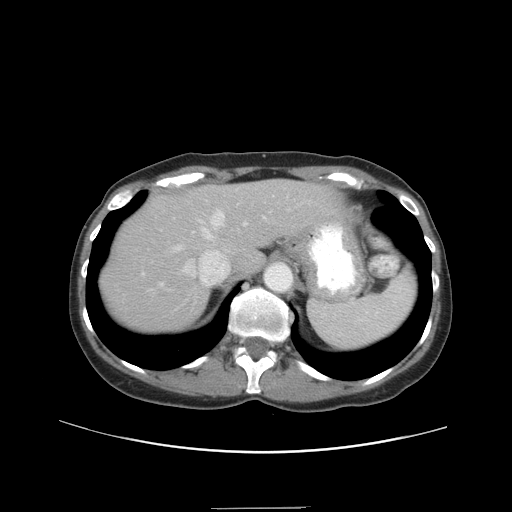
Contrast-enhanced abdominal CT, one axial slice. Slice 30 of 38 in the series (ordered by position). Intravenous contrast given. Soft-tissue window (W 400 / L 40 HU). 512 × 512 image matrix, field of view 388 × 388 mm. Female patient, age 64 years. Case-level facts recorded for this patient, not image findings: diagnosis: colorectal cancer liver metastases, imaged before liver resection; multiple liver metastases: no; largest metastasis: 3.8 cm.
Outlined on this slice (manually delineated by an expert):
- hepatic veins: box from (x=149, y=210) to (x=247, y=291) px
- liver: (x=103, y=182)–(x=338, y=331)
- planned liver remnant (the part of the liver to remain after resection): (x=147, y=182)–(x=338, y=268)
- portal vein (with intrahepatic branches): (x=143, y=216)–(x=265, y=275)